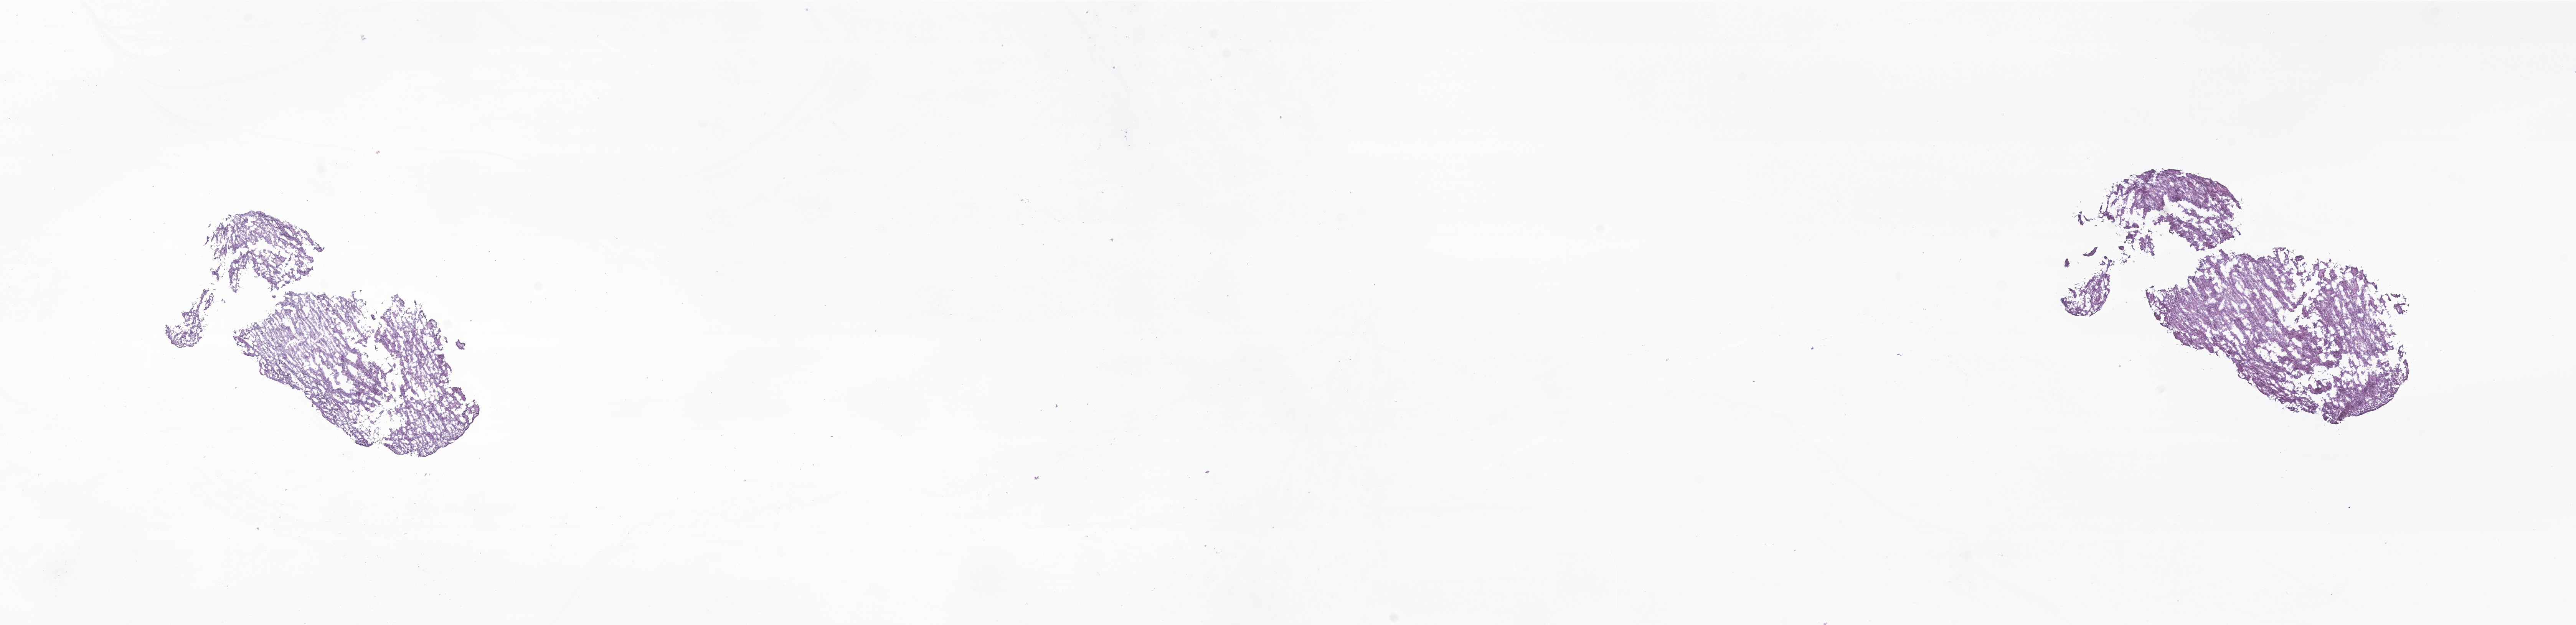
Whole-slide image, haematoxylin and eosin stain of tumor tissue from the innominate bone and/or sacrum and/or coccyx, shown as a low-resolution overview of the whole scanned area (about 28.3 x 6.9 mm), frozen section. Female patient, age 206 months (17 years 2 months).
- tissue or organ of origin (case record): pelvic bones, sacrum, coccyx and associated joints
- recorded diagnosis: Mesenchymal chondrosarcoma